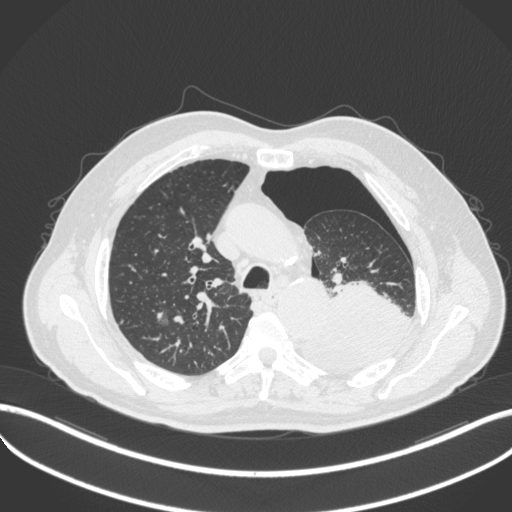
Chest CT, one axial slice; slice 362 of 466 in the series (ordered by position); reconstruction kernel B31f; 120 kVp; lung window (W 1500 / L -600 HU); 512 × 512 image matrix, field of view 400 × 400 mm. Patient: male, 76 years. Case-level facts recorded for this patient, not image findings: clinical TNM (as recorded): T3 N0 M1b.
Outlined on this slice (bounding box drawn by a radiologist):
- lung tumour (recorded histology: adenocarcinoma): bounding box [x1, y1, x2, y2] px = [299, 282, 419, 365]